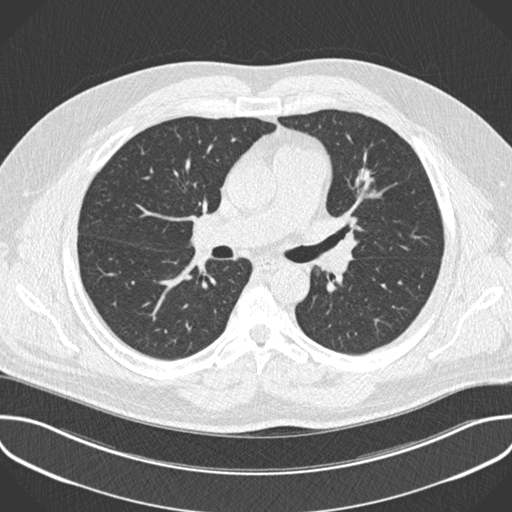
Low-dose screening chest CT, one axial slice. Slice 127 of 201 in the series (ordered by position). 120 kVp. Lung window (W 1500 / L -600 HU). 2 mm slice thickness. 512 × 512 image matrix, field of view 386 × 386 mm.
Structures marked on this image (outlined manually by an expert reader):
- lesion 1 (tumor, upper lobe of left lung): box from (x=356, y=169) to (x=373, y=186) px